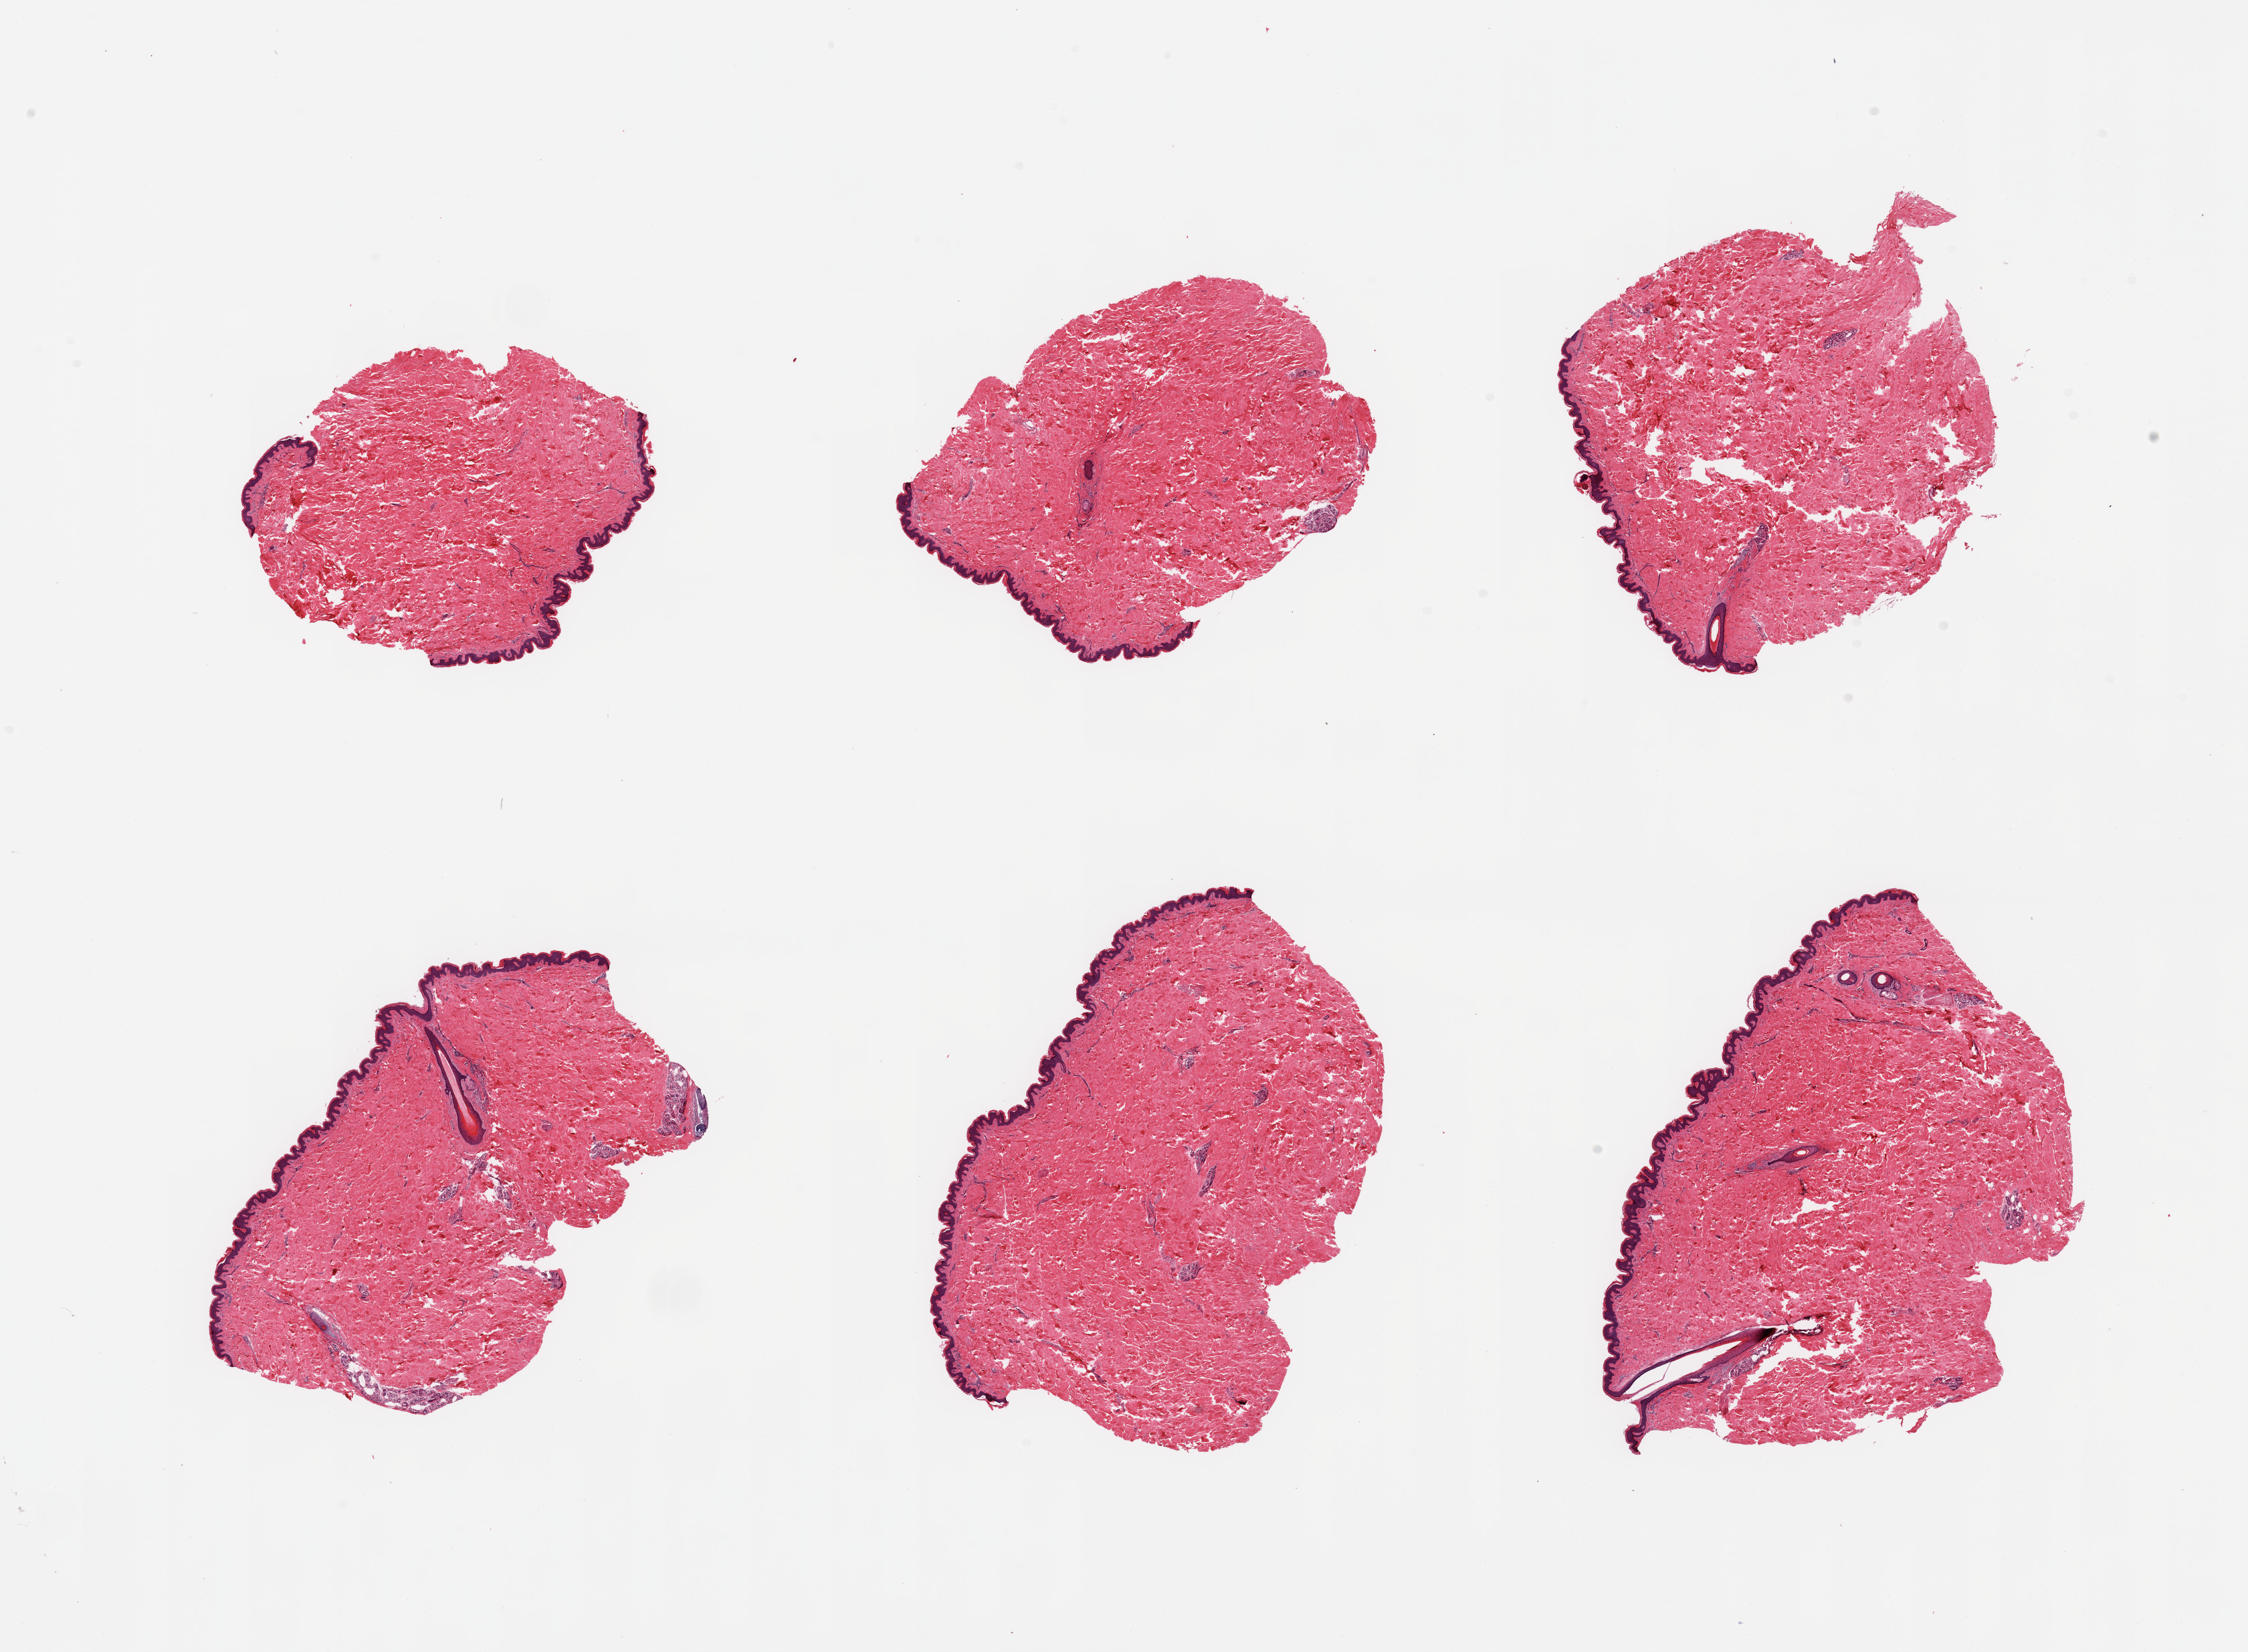
Digitized H&E-stained section, shown as a low-resolution overview of the whole scanned area (about 26.6 x 19.5 mm); PAXgene-fixed, paraffin-embedded tissue; sampled site (target tissue): skin of suprapubic region; tissue donor sample. Donor sex: male.
Pathologist's review note for this sample: 6 pieces; well trimmed hair bearing skin.